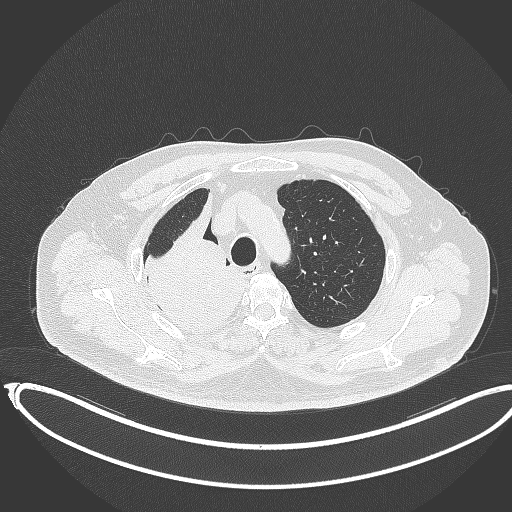
Chest CT, one axial slice; position 290 of 403 along the scan axis; reconstruction kernel B70f; lung window (W 1500 / L -600 HU); 1 mm slice thickness; 512 × 512 image matrix, field of view 436 × 436 mm. Patient: male, 68 years. Case-level facts recorded for this patient, not image findings: clinical TNM (as recorded): T2a N0 M0.
Annotated regions visible in this slice (rectangle marked by the reading radiologist):
- lung tumour (recorded histology: adenocarcinoma): box from (x=132, y=194) to (x=247, y=335) px